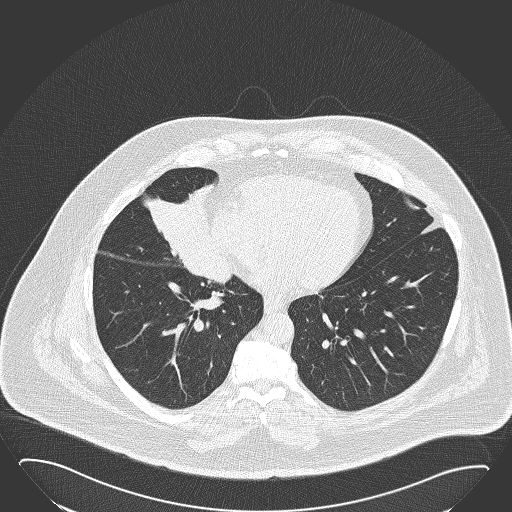
Low-dose screening chest CT, one axial slice; slice 68 of 168 in the series (ordered by position); lung window (W 1500 / L -600 HU); 512 × 512 image matrix, field of view 432 × 432 mm.
Annotated regions visible in this slice (outlined manually by an expert reader):
- lesion 1 (tumor, hilum of right lung): bounding box (x1, y1, x2, y2) in pixels: (146, 184, 232, 284)